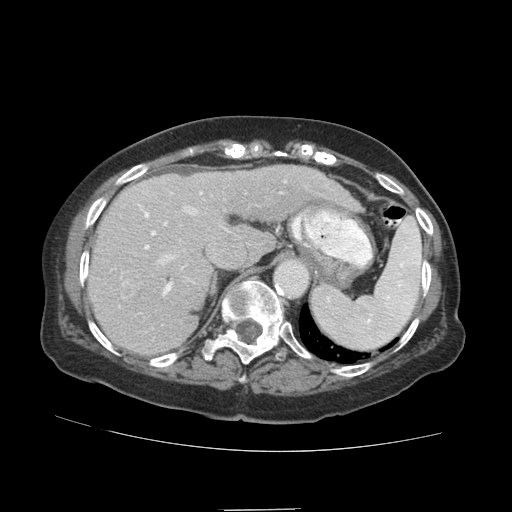
Contrast-enhanced abdominal CT (liver protocol), one axial slice; position 66 of 89 along the scan axis; soft-tissue window (W 400 / L 40 HU); 512 × 512 image matrix, field of view 360 × 360 mm. From the clinical record (not read from this slice): diagnosis: hepatocellular carcinoma (patient treated with transarterial chemoembolisation; whether this scan precedes or follows treatment is not stated here); TNM stage (as recorded): Stage-II; Child-Pugh class: A; tumour differentiation: moderately differentiated; tumour nodularity: multinodular.
Structures marked on this image (semi-automatic segmentation, software-assisted and operator-edited):
- liver parenchyma outside the tumour (the mass and vessels are separate outlines, so this box may not span the whole liver): bounding box <88,166,315,354> (left, top, right, bottom; pixels)
- liver vessels: <118,180,287,314>